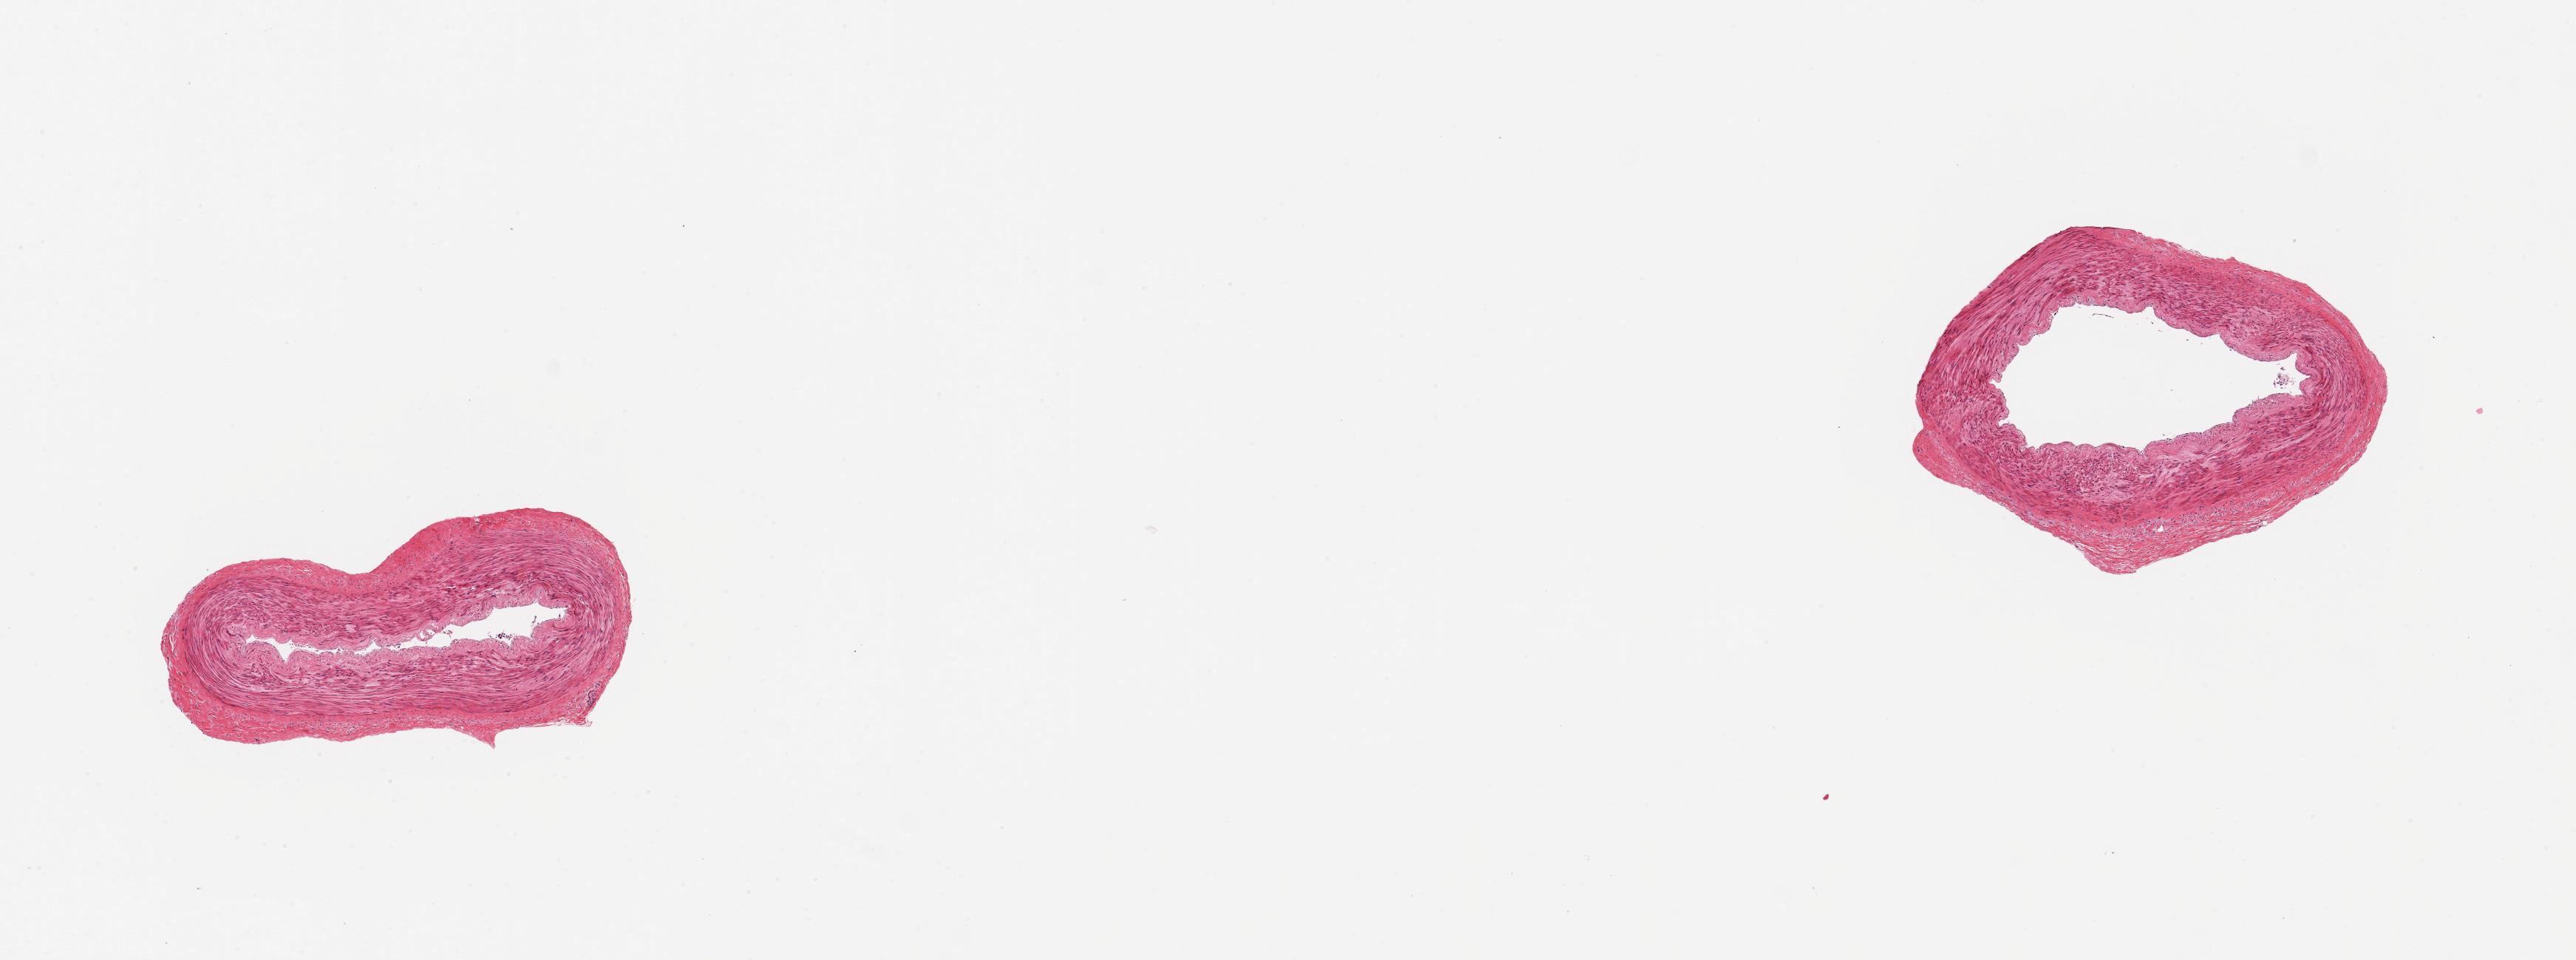
Whole-slide image, hematoxylin and eosin (H&E) stain, low-resolution overview of the scanned area, about 13.8 x 5.1 mm (acquisition: 20x scan), PAXgene-fixed, paraffin-embedded tissue, target tissue: tibial artery, donor tissue sample.
Pathologist's review note for this sample: 2 pieces; well trimmed.